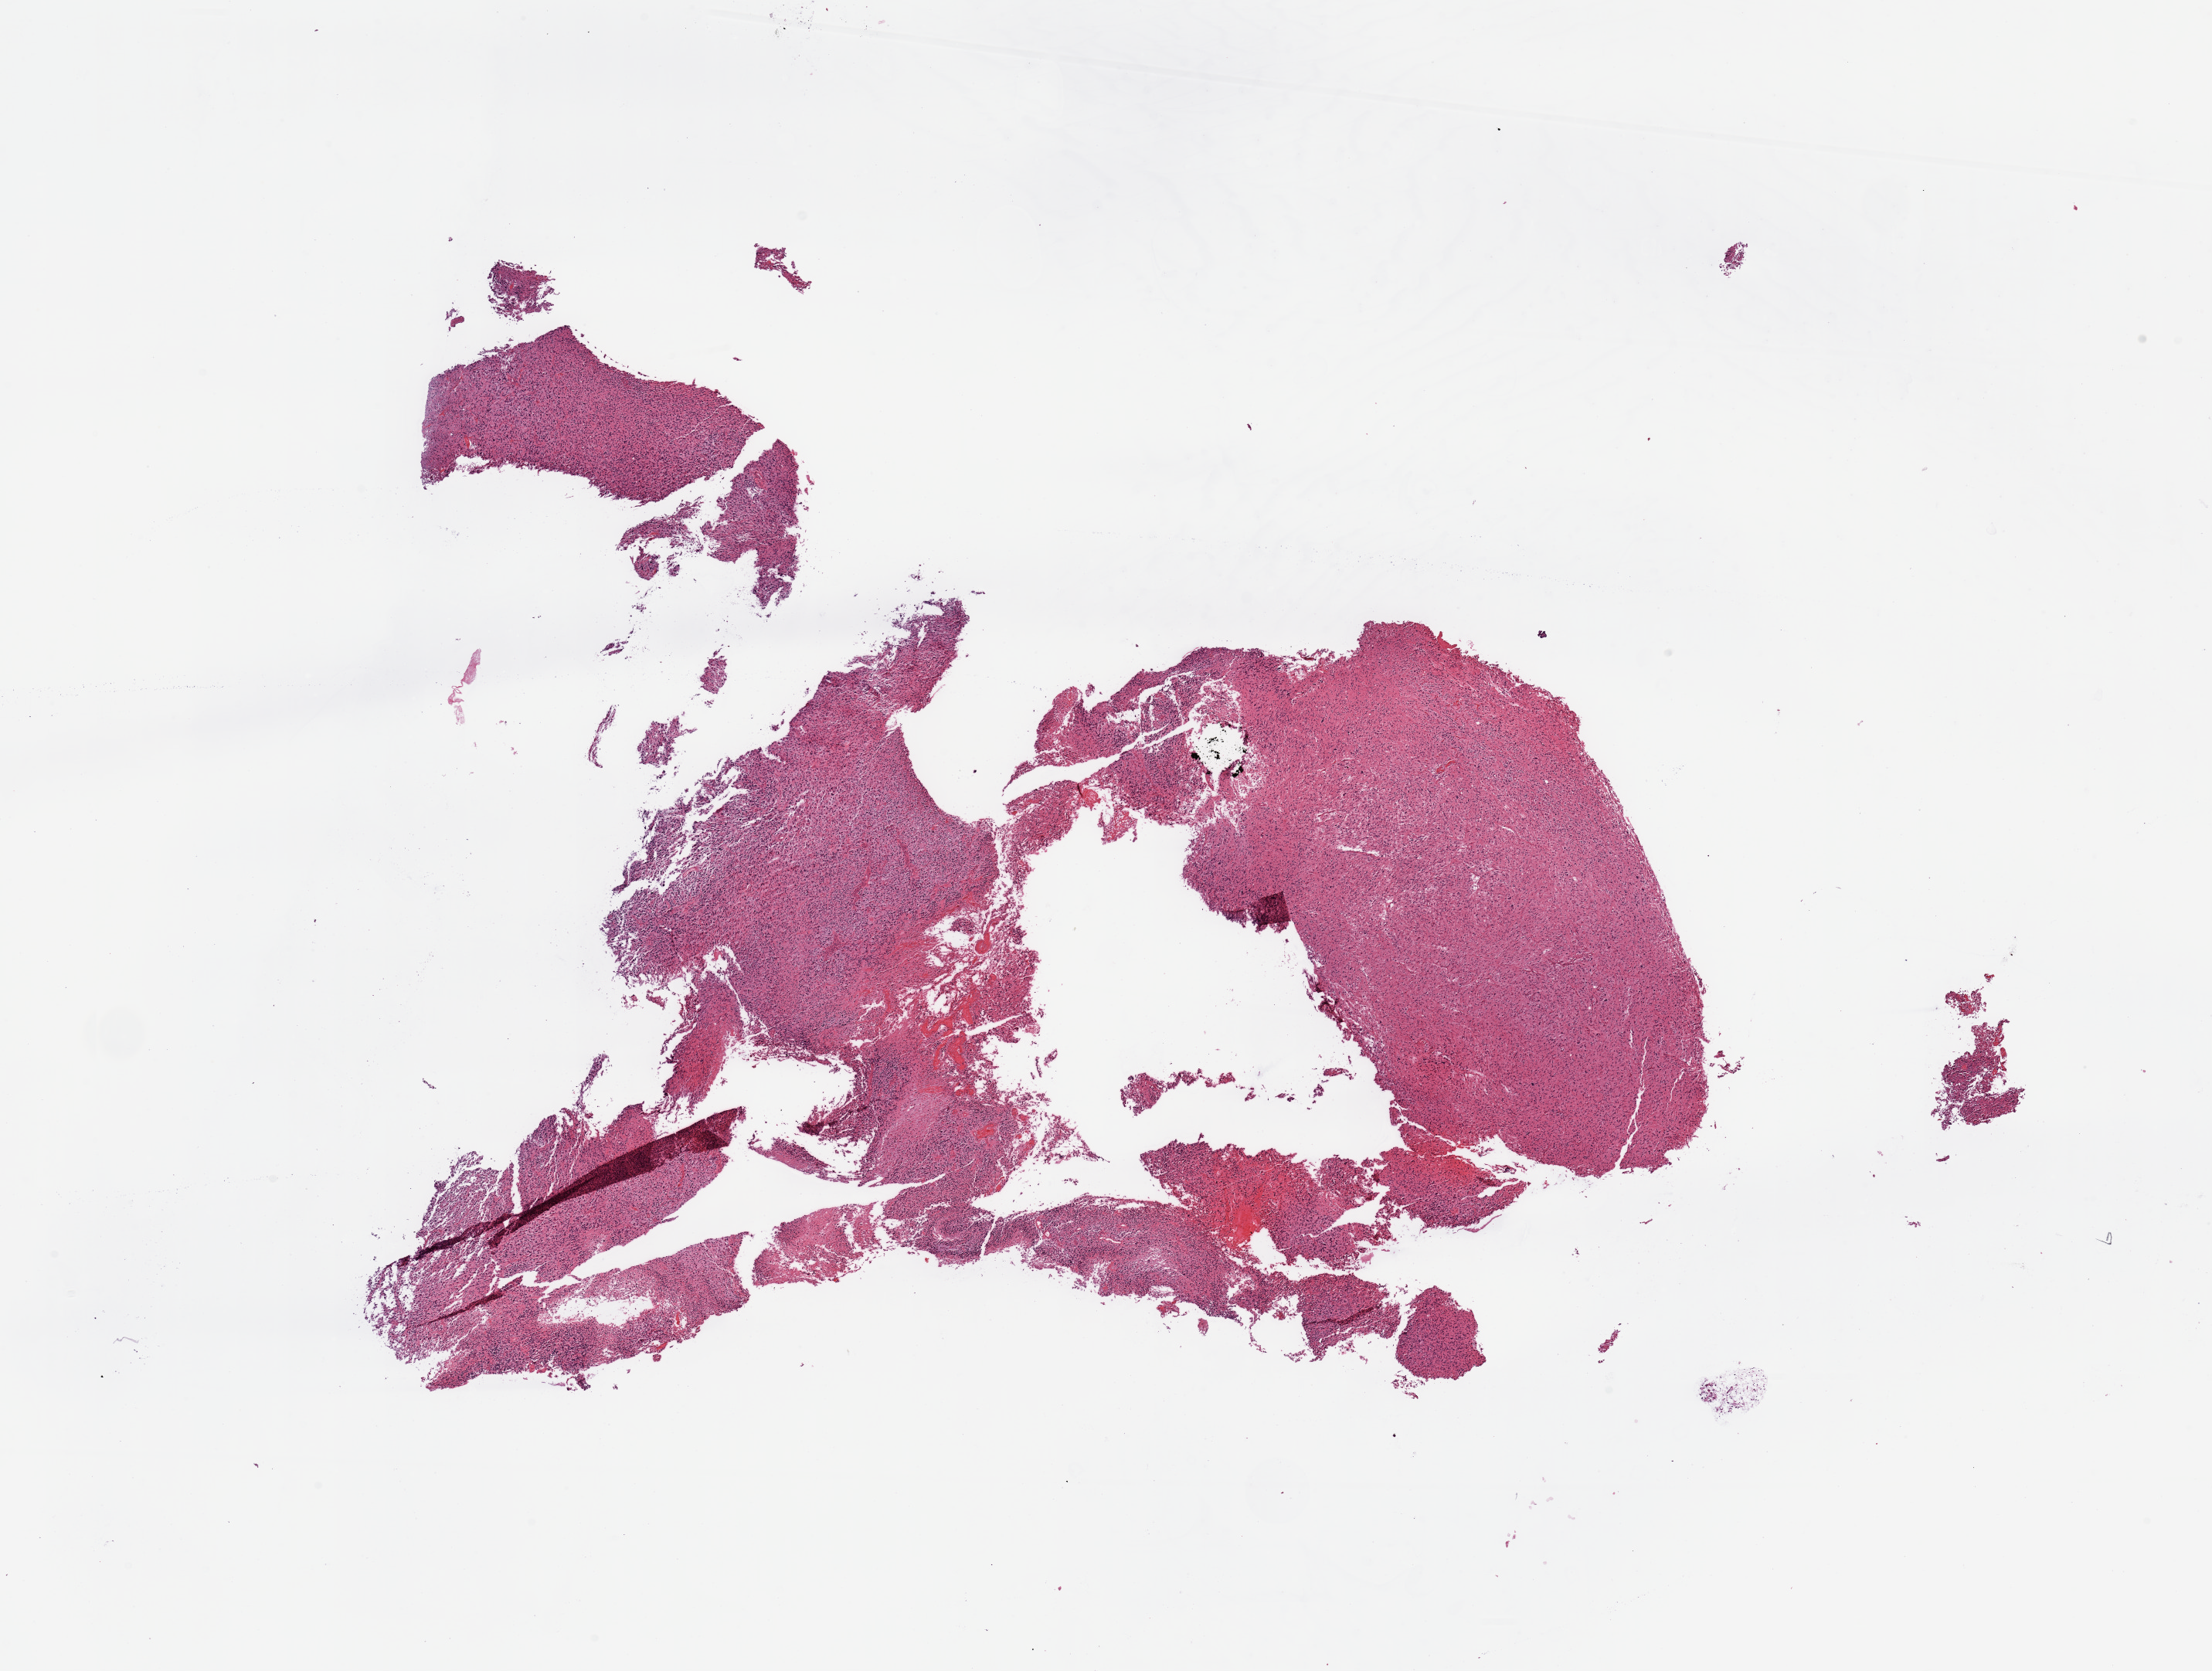
Hematoxylin and eosin (H&E) stained whole-slide image, shown as a low-resolution overview of the whole scanned area (about 22.6 x 17.1 mm, from a 20x scan), brain, tumour tissue. Patient: male, age 70 years.
• patient diagnosis (cohort enrolment): glioblastoma multiforme (brain)
• primary tumour site (as recorded): parietal lobe